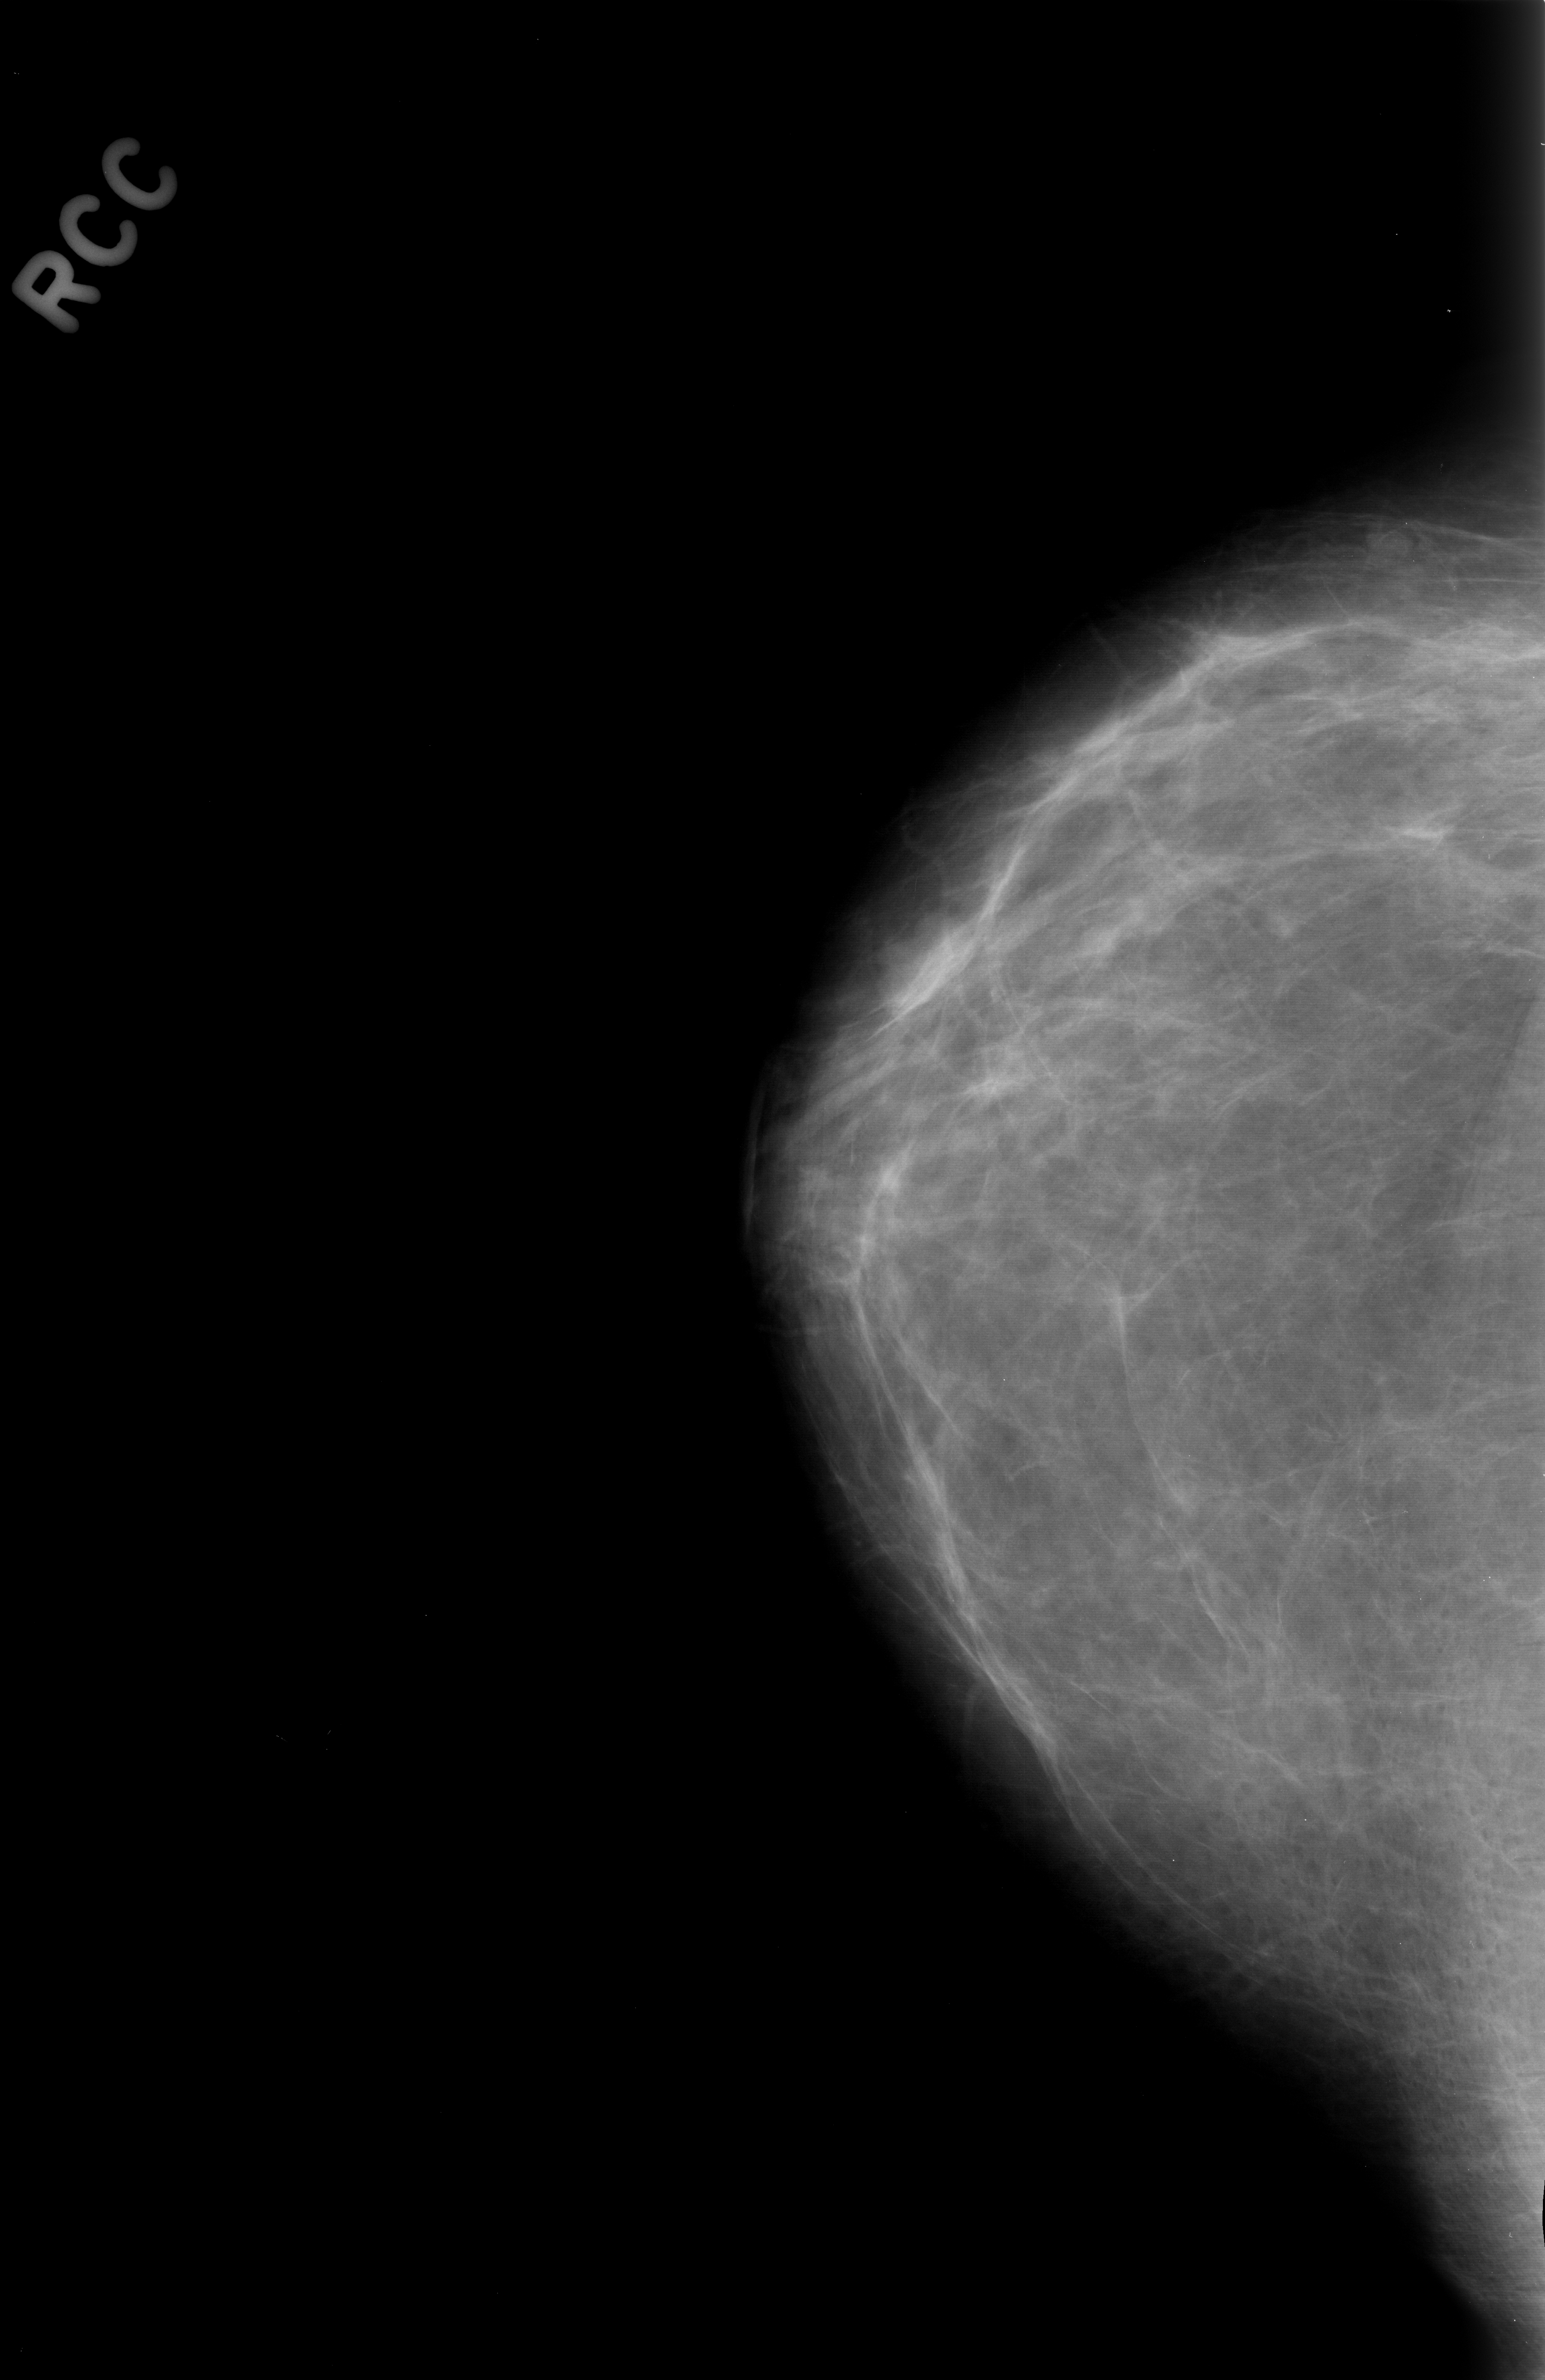
Scanned film-screen mammogram. Right breast. CC view. Breast composition: almost entirely fatty (BI-RADS density category 1 of 4). 1545 × 2380 image matrix.
Expert-marked regions of interest on this film, with their recorded descriptors:
- mass, shape lobulated, margins circumscribed; BI-RADS assessment category 3; subtlety rating 5 on a 1 (subtle) to 5 (obvious) scale; pathology (as recorded): benign: bounding box (x1, y1, x2, y2) in pixels: (857, 905, 993, 1061)